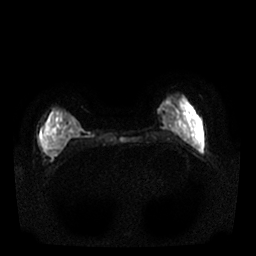
Breast MRI, one axial slice. Slice 7 of 25 in the series (ordered by position). Diffusion-weighted series; image 2 of 4 stored at this slice position (different b-values; order by instance number). 1.5 T. 4 mm slice thickness. 256 × 256 image matrix. Female patient.
Structures marked on this image (manually delineated by an expert):
- tumour on diffusion-weighted imaging: bounding box <43,129,52,157> (left, top, right, bottom; pixels)